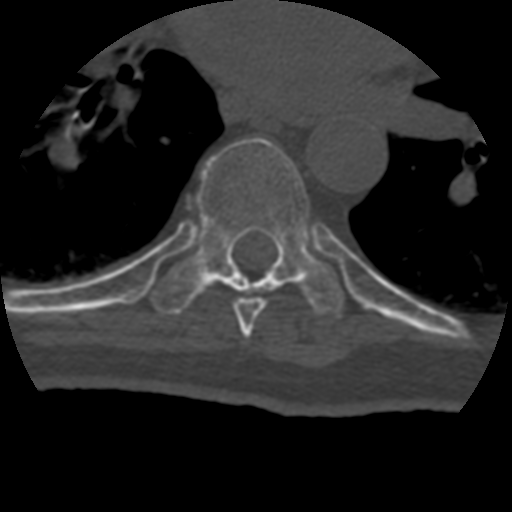
CT including the spine, one axial slice. Position 268 of 399 along the scan axis. 120 kVp. Bone window (W 1800 / L 400 HU). 1.25 mm slice thickness. 512 × 512 image matrix, field of view 160 × 160 mm. Patient age 69 years. From the clinical record (not read from this slice): primary cancer: prostate.
Annotated regions visible in this slice (semi-automatically segmented with operator editing):
- T7 vertebra: box from (x=234, y=297) to (x=266, y=337) px
- T8 vertebra: (x=149, y=137)–(x=346, y=320)